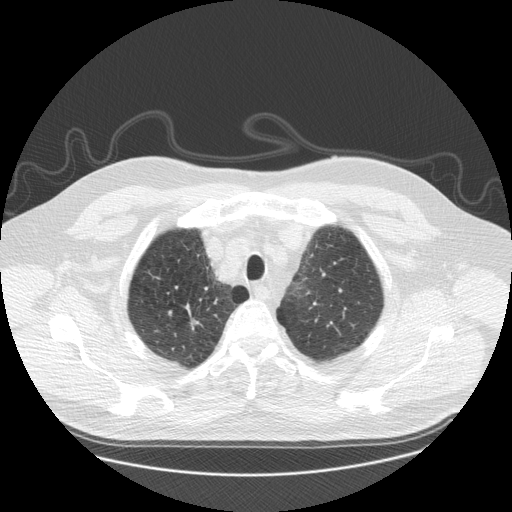
Low-dose screening chest CT, axial slice; third screening round (two years after baseline); lung window (W 1500 / L -600 HU); 2.5 mm slice thickness; standard (soft-tissue) reconstruction kernel (STANDARD). Male, age 61 years at enrolment.
Lesion marked by an expert reader, box from (x=176, y=306) to (x=211, y=341) px. Reader record for this screening exam (exam-level; its link to the box is not recorded): non-calcified nodule or mass ≥4 mm, right upper lobe, 10 × 7 mm, smooth margins, soft tissue attenuation, pre-existing on the prior screen: yes; interval growth: yes. Official screen result: positive, other. Participant outcome: lung cancer diagnosed 110 days after this screen — squamous cell carcinoma, NOS, right upper lobe, moderately differentiated (G2), stage IA (AJCC 6th edition), 10 mm at pathology.